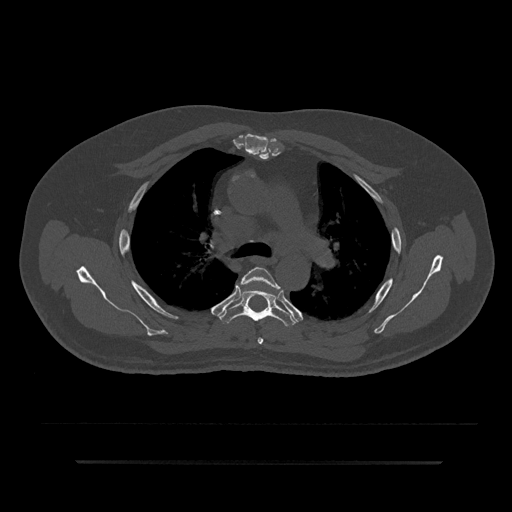
CT including the spine, one axial slice. Position 588 of 797 along the scan axis. 120 kVp. Bone window (W 1800 / L 400 HU). 0.5 mm slice thickness. 512 × 512 image matrix, field of view 464 × 464 mm. Patient: male, 59 years. From the clinical record (not read from this slice): primary cancer: bile ducts; vertebrae with lytic lesions (as recorded): T10.
Outlined on this slice (semi-automatically segmented with operator editing):
- T4 vertebra: box from (x=240, y=267) to (x=281, y=345) px
- T5 vertebra: (x=219, y=289)–(x=297, y=326)